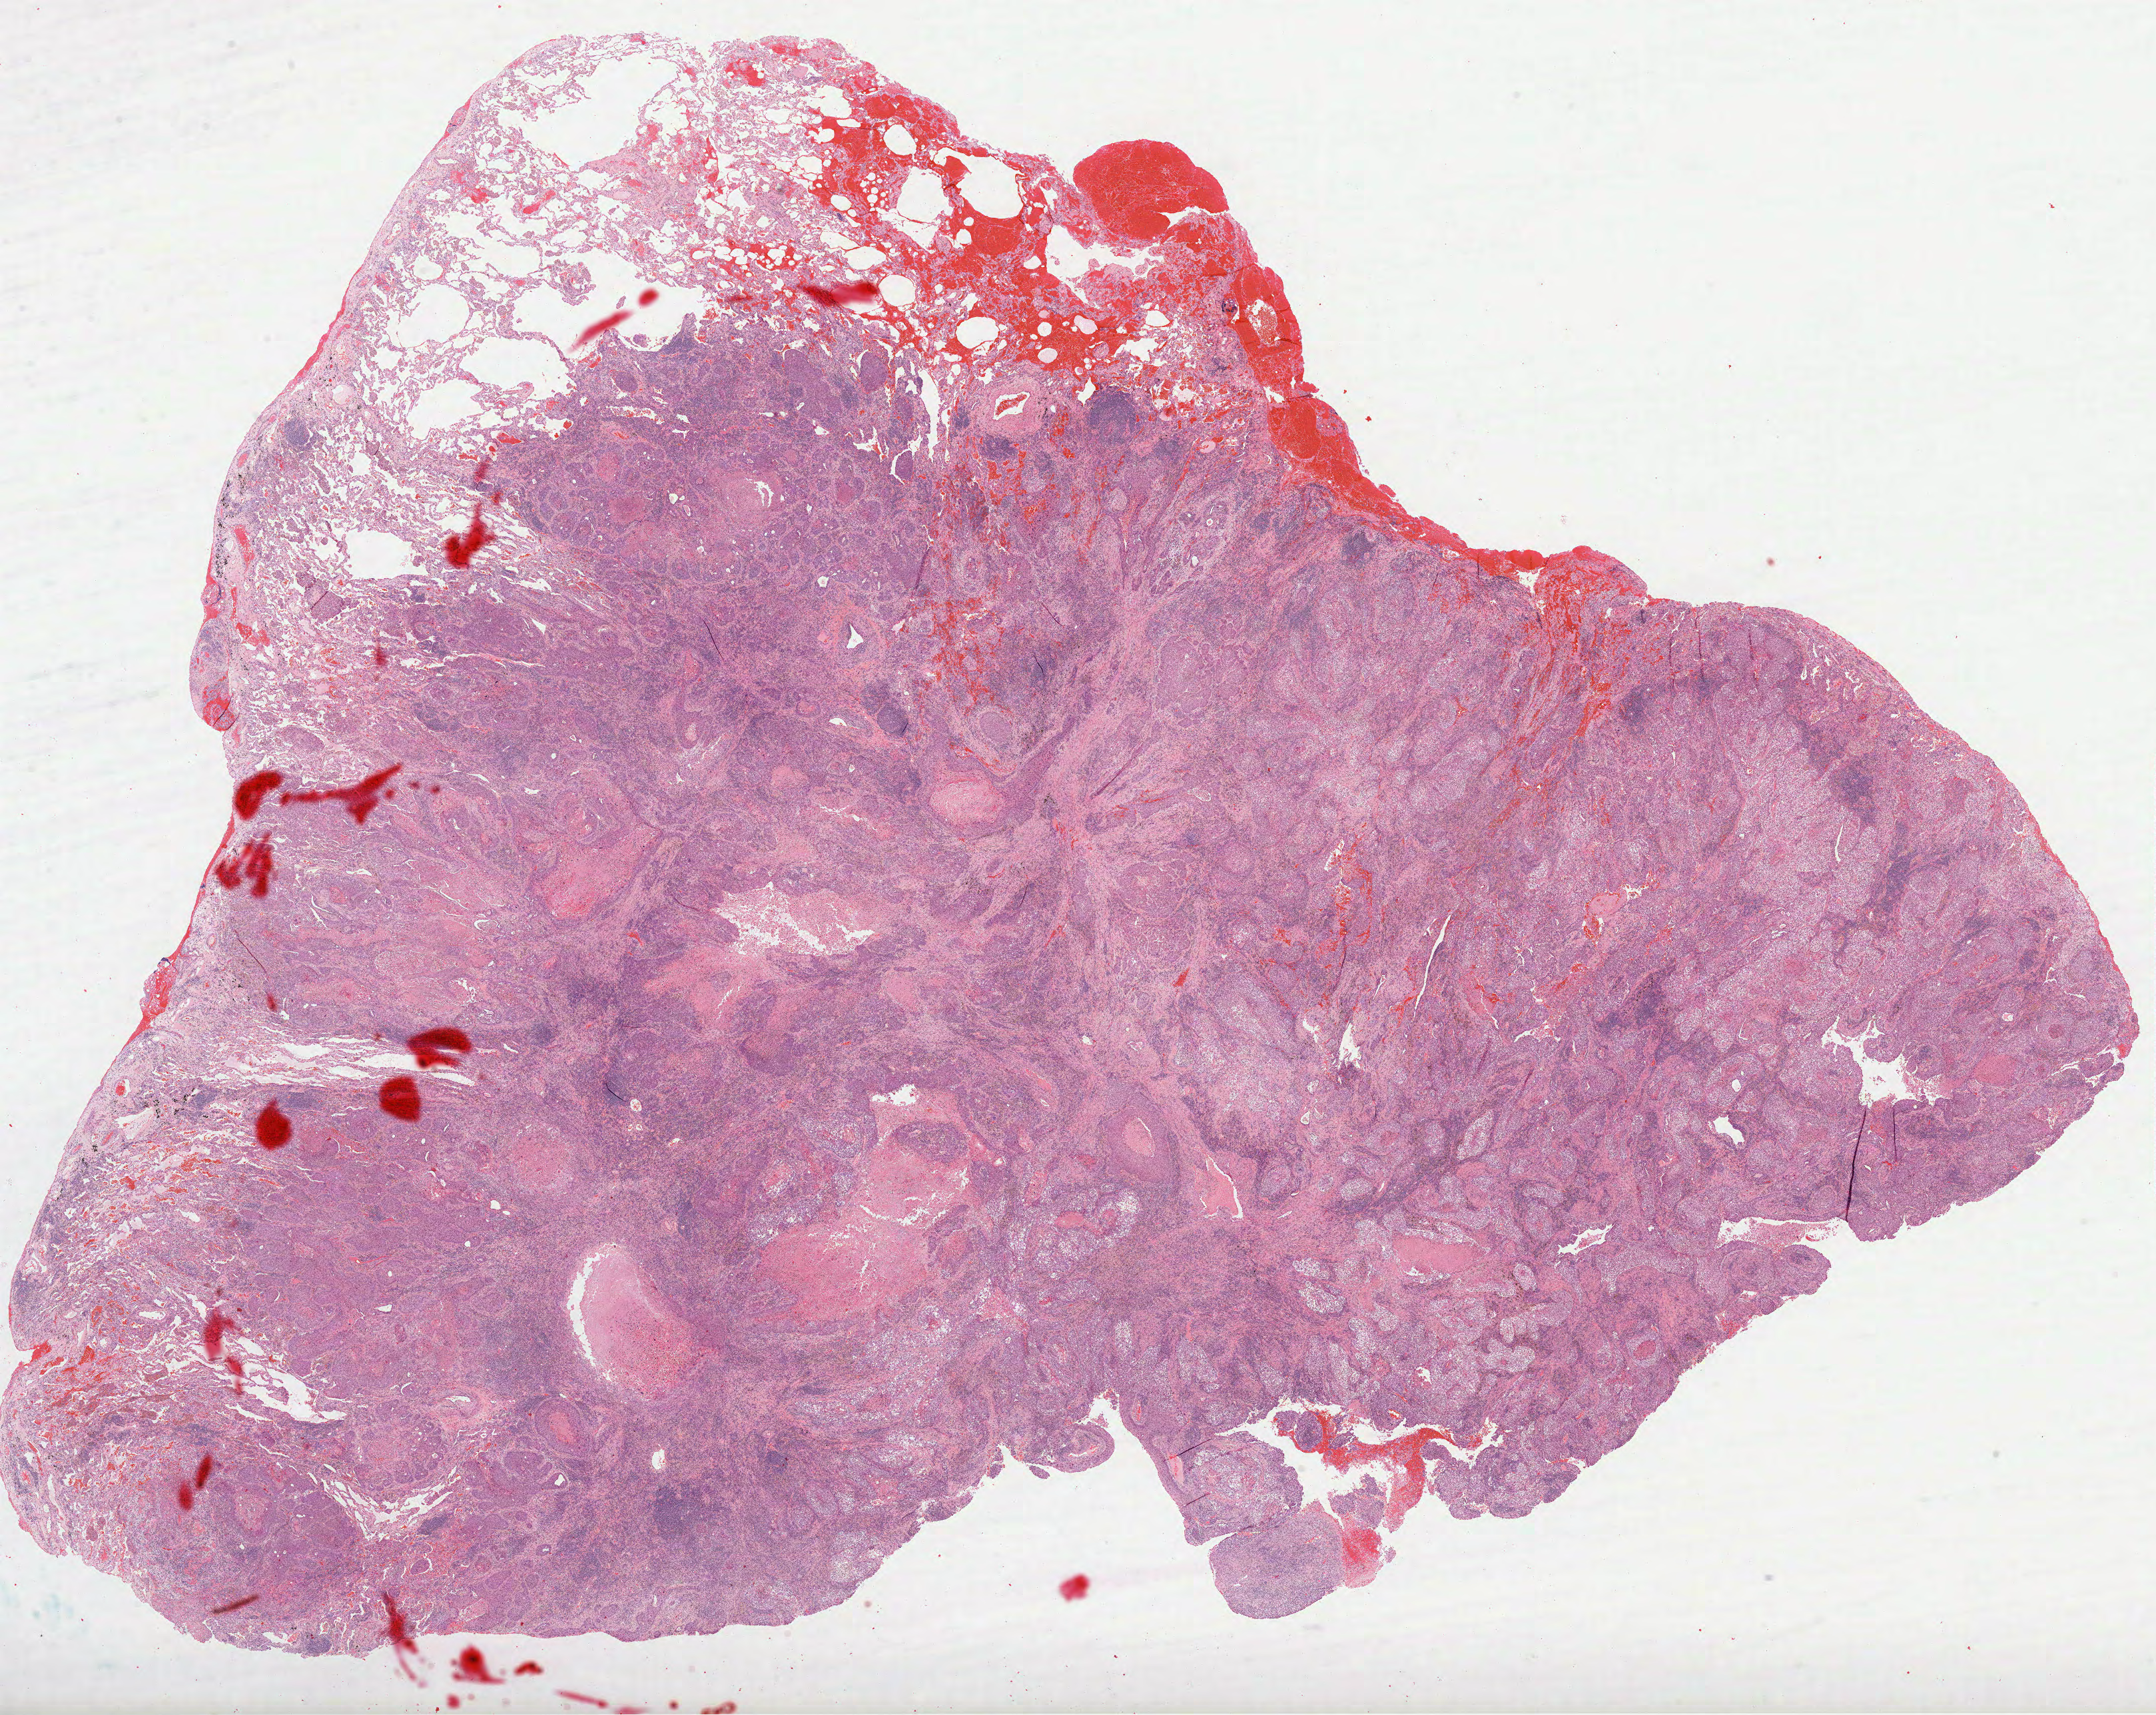
Digitized H&E tissue section (whole slide) — a low-resolution overview of the entire scanned area, about 26.1 x 20.8 mm; FFPE section; lung, primary tumour sample. Patient: female, age at initial diagnosis 52 years.
AJCC pathologic stage: IB (7th edition). Laterality: right. Histologic diagnosis: Squamous cell carcinoma, NOS.